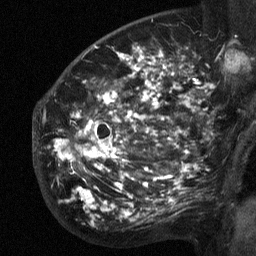
Breast MRI (dynamic contrast-enhanced), one sagittal slice. Position 39 of 64 along the scan axis. Dynamic contrast-enhanced study with each time point stored as its own series, time point 2 of 3 at this slice position (early post-contrast, ordered by acquisition time). 1.5 T. TE 4.8 ms, TR 27 ms. 2.3 mm slice thickness. 256 × 256 image matrix. Female patient, age 50 years. Case-level facts recorded for this patient, not image findings: setting: breast cancer imaged before/during neoadjuvant chemotherapy; receptor status: HER2-positive.
Structures marked on this image (semi-automatically segmented with operator editing):
- analysis volume of interest (the breast-tissue region the enhancement analysis was run in; not a lesion): bounding box [x1, y1, x2, y2] px = [53, 64, 211, 218]
- tumour enhancement mask (voxels above the 90 % enhancement threshold inside the analysis volume of interest): [55, 65, 187, 214]